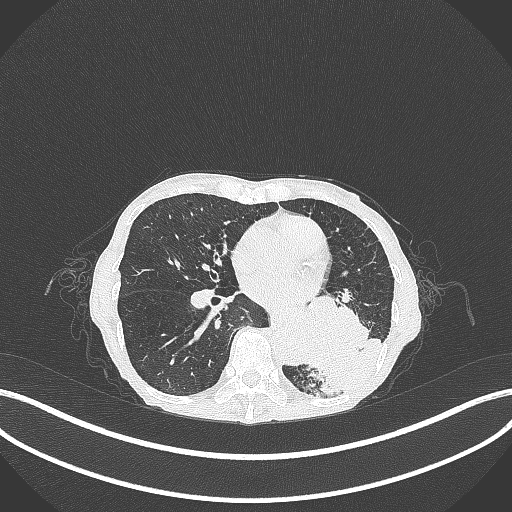
Chest CT, one axial slice; position 120 of 347 along the scan axis; 120 kVp; lung window (W 1500 / L -600 HU); 512 × 512 image matrix, field of view 400 × 400 mm. Female patient, age 70 years. From the clinical record (not read from this slice): clinical TNM (as recorded): T3 N0 M0.
Structures marked on this image (rectangle marked by the reading radiologist):
- lung tumour (recorded histology: small cell carcinoma): bounding box (x1, y1, x2, y2) in pixels: (293, 304, 373, 389)